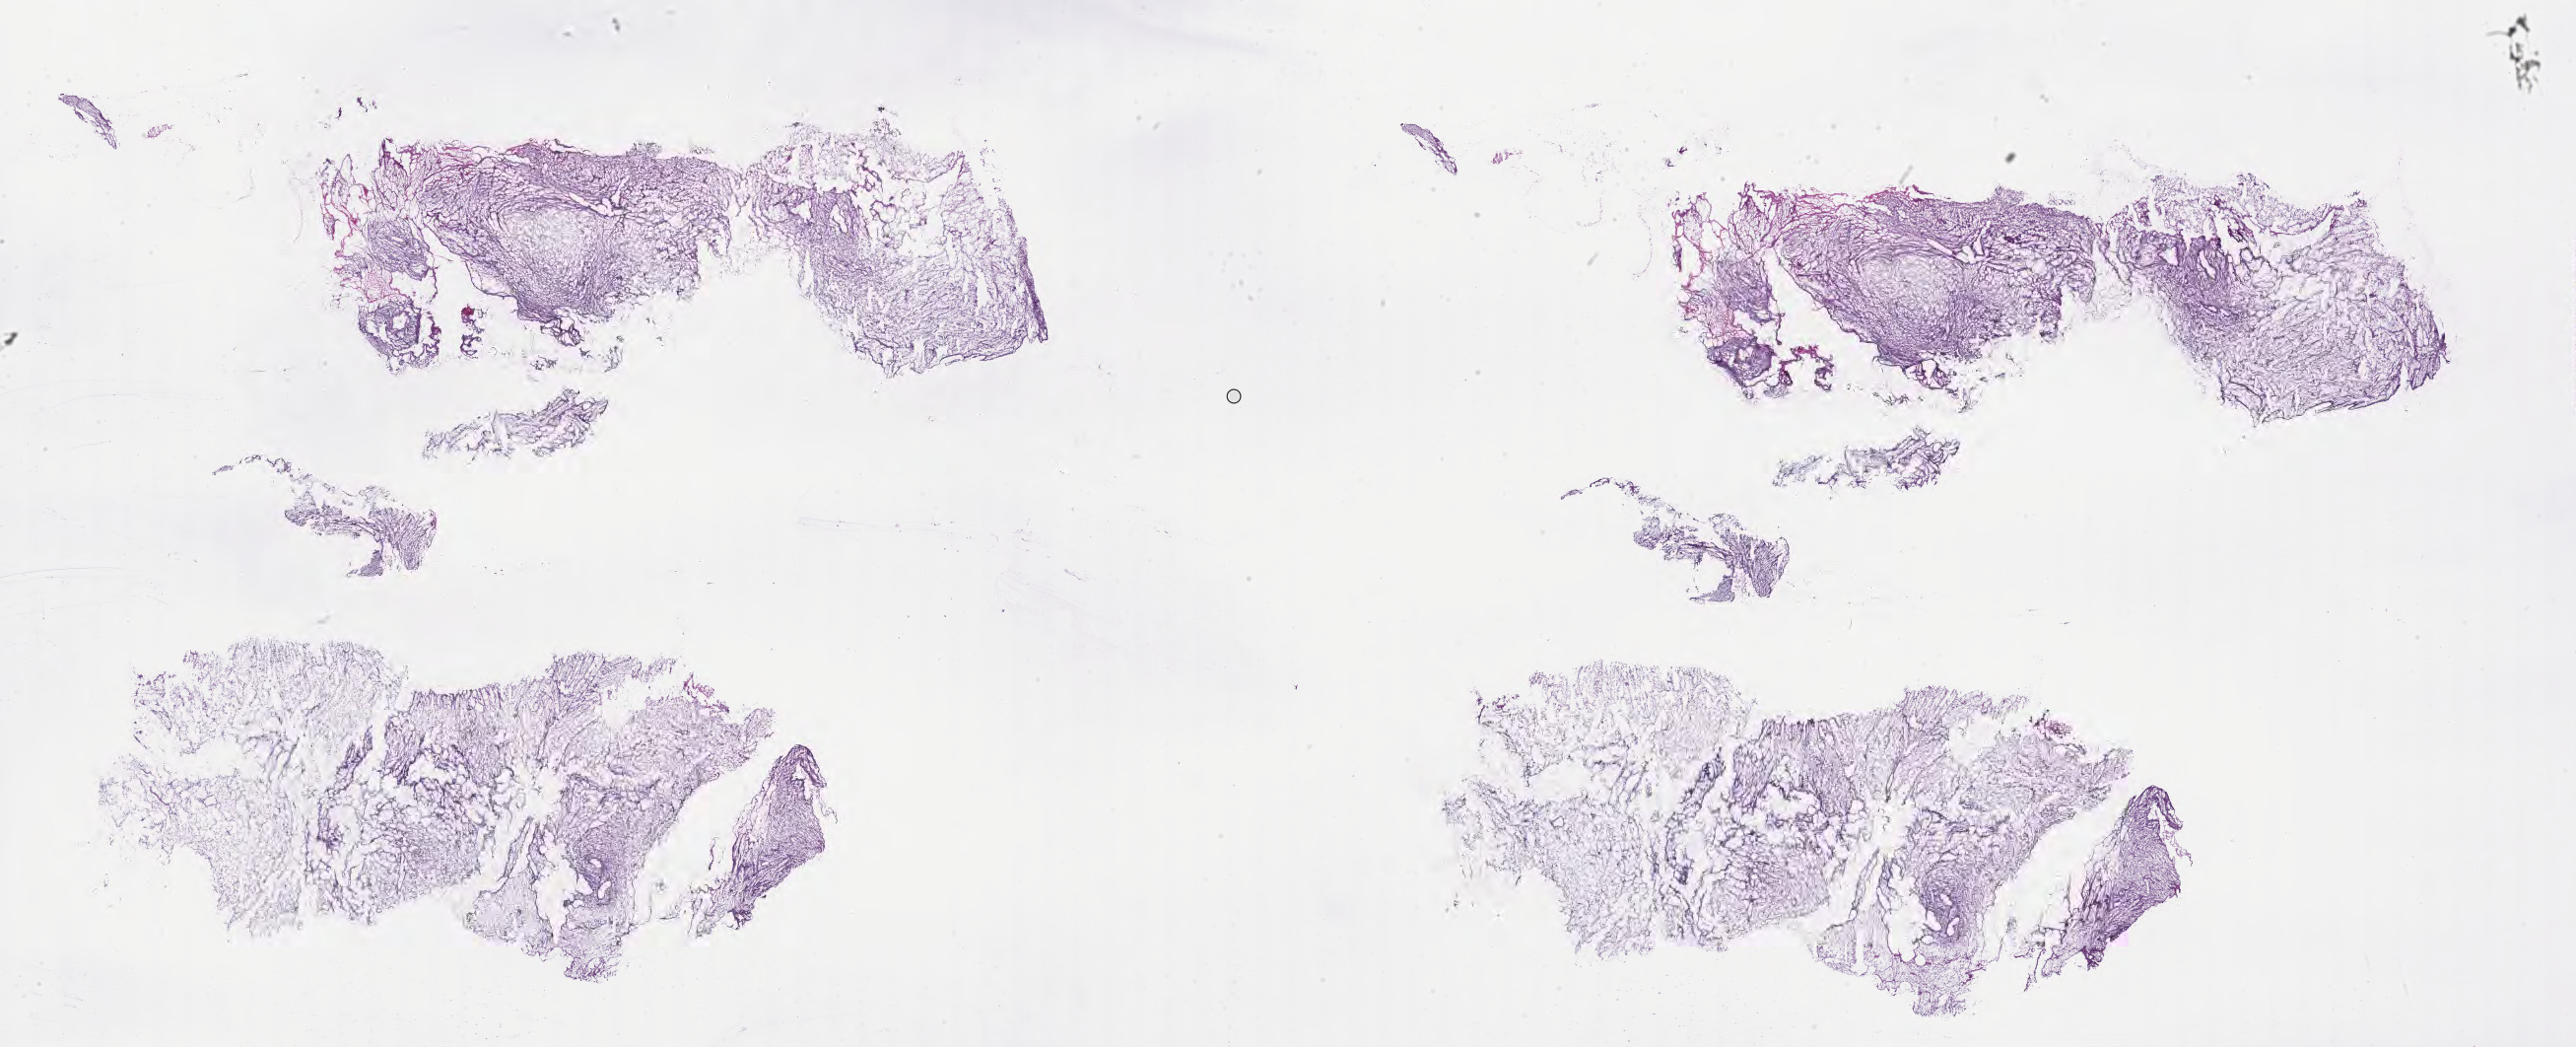
Whole-slide image, haematoxylin and eosin stain of tumor tissue from the retroperitoneum — a low-resolution overview of the entire scanned area, about 42.3 x 17.2 mm; cryosection (OCT / tissue freezing medium). Patient: male, age 54 months (4 years 6 months).
Recorded diagnosis: Embryonal rhabdomyosarcoma, NOS.